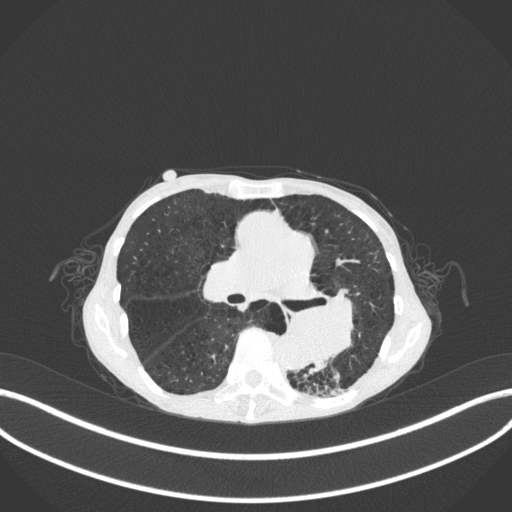
Chest CT, one axial slice; slice 157 of 347 in the series (ordered by position); lung window (W 1500 / L -600 HU); 1 mm slice thickness; 512 × 512 image matrix. Female patient, age 70 years. From the clinical record (not read from this slice): clinical TNM (as recorded): T3 N0 M0.
Outlined on this slice (rectangle marked by the reading radiologist):
- lung tumour (recorded histology: small cell carcinoma): bounding box (x1, y1, x2, y2) in pixels: (286, 289, 365, 373)